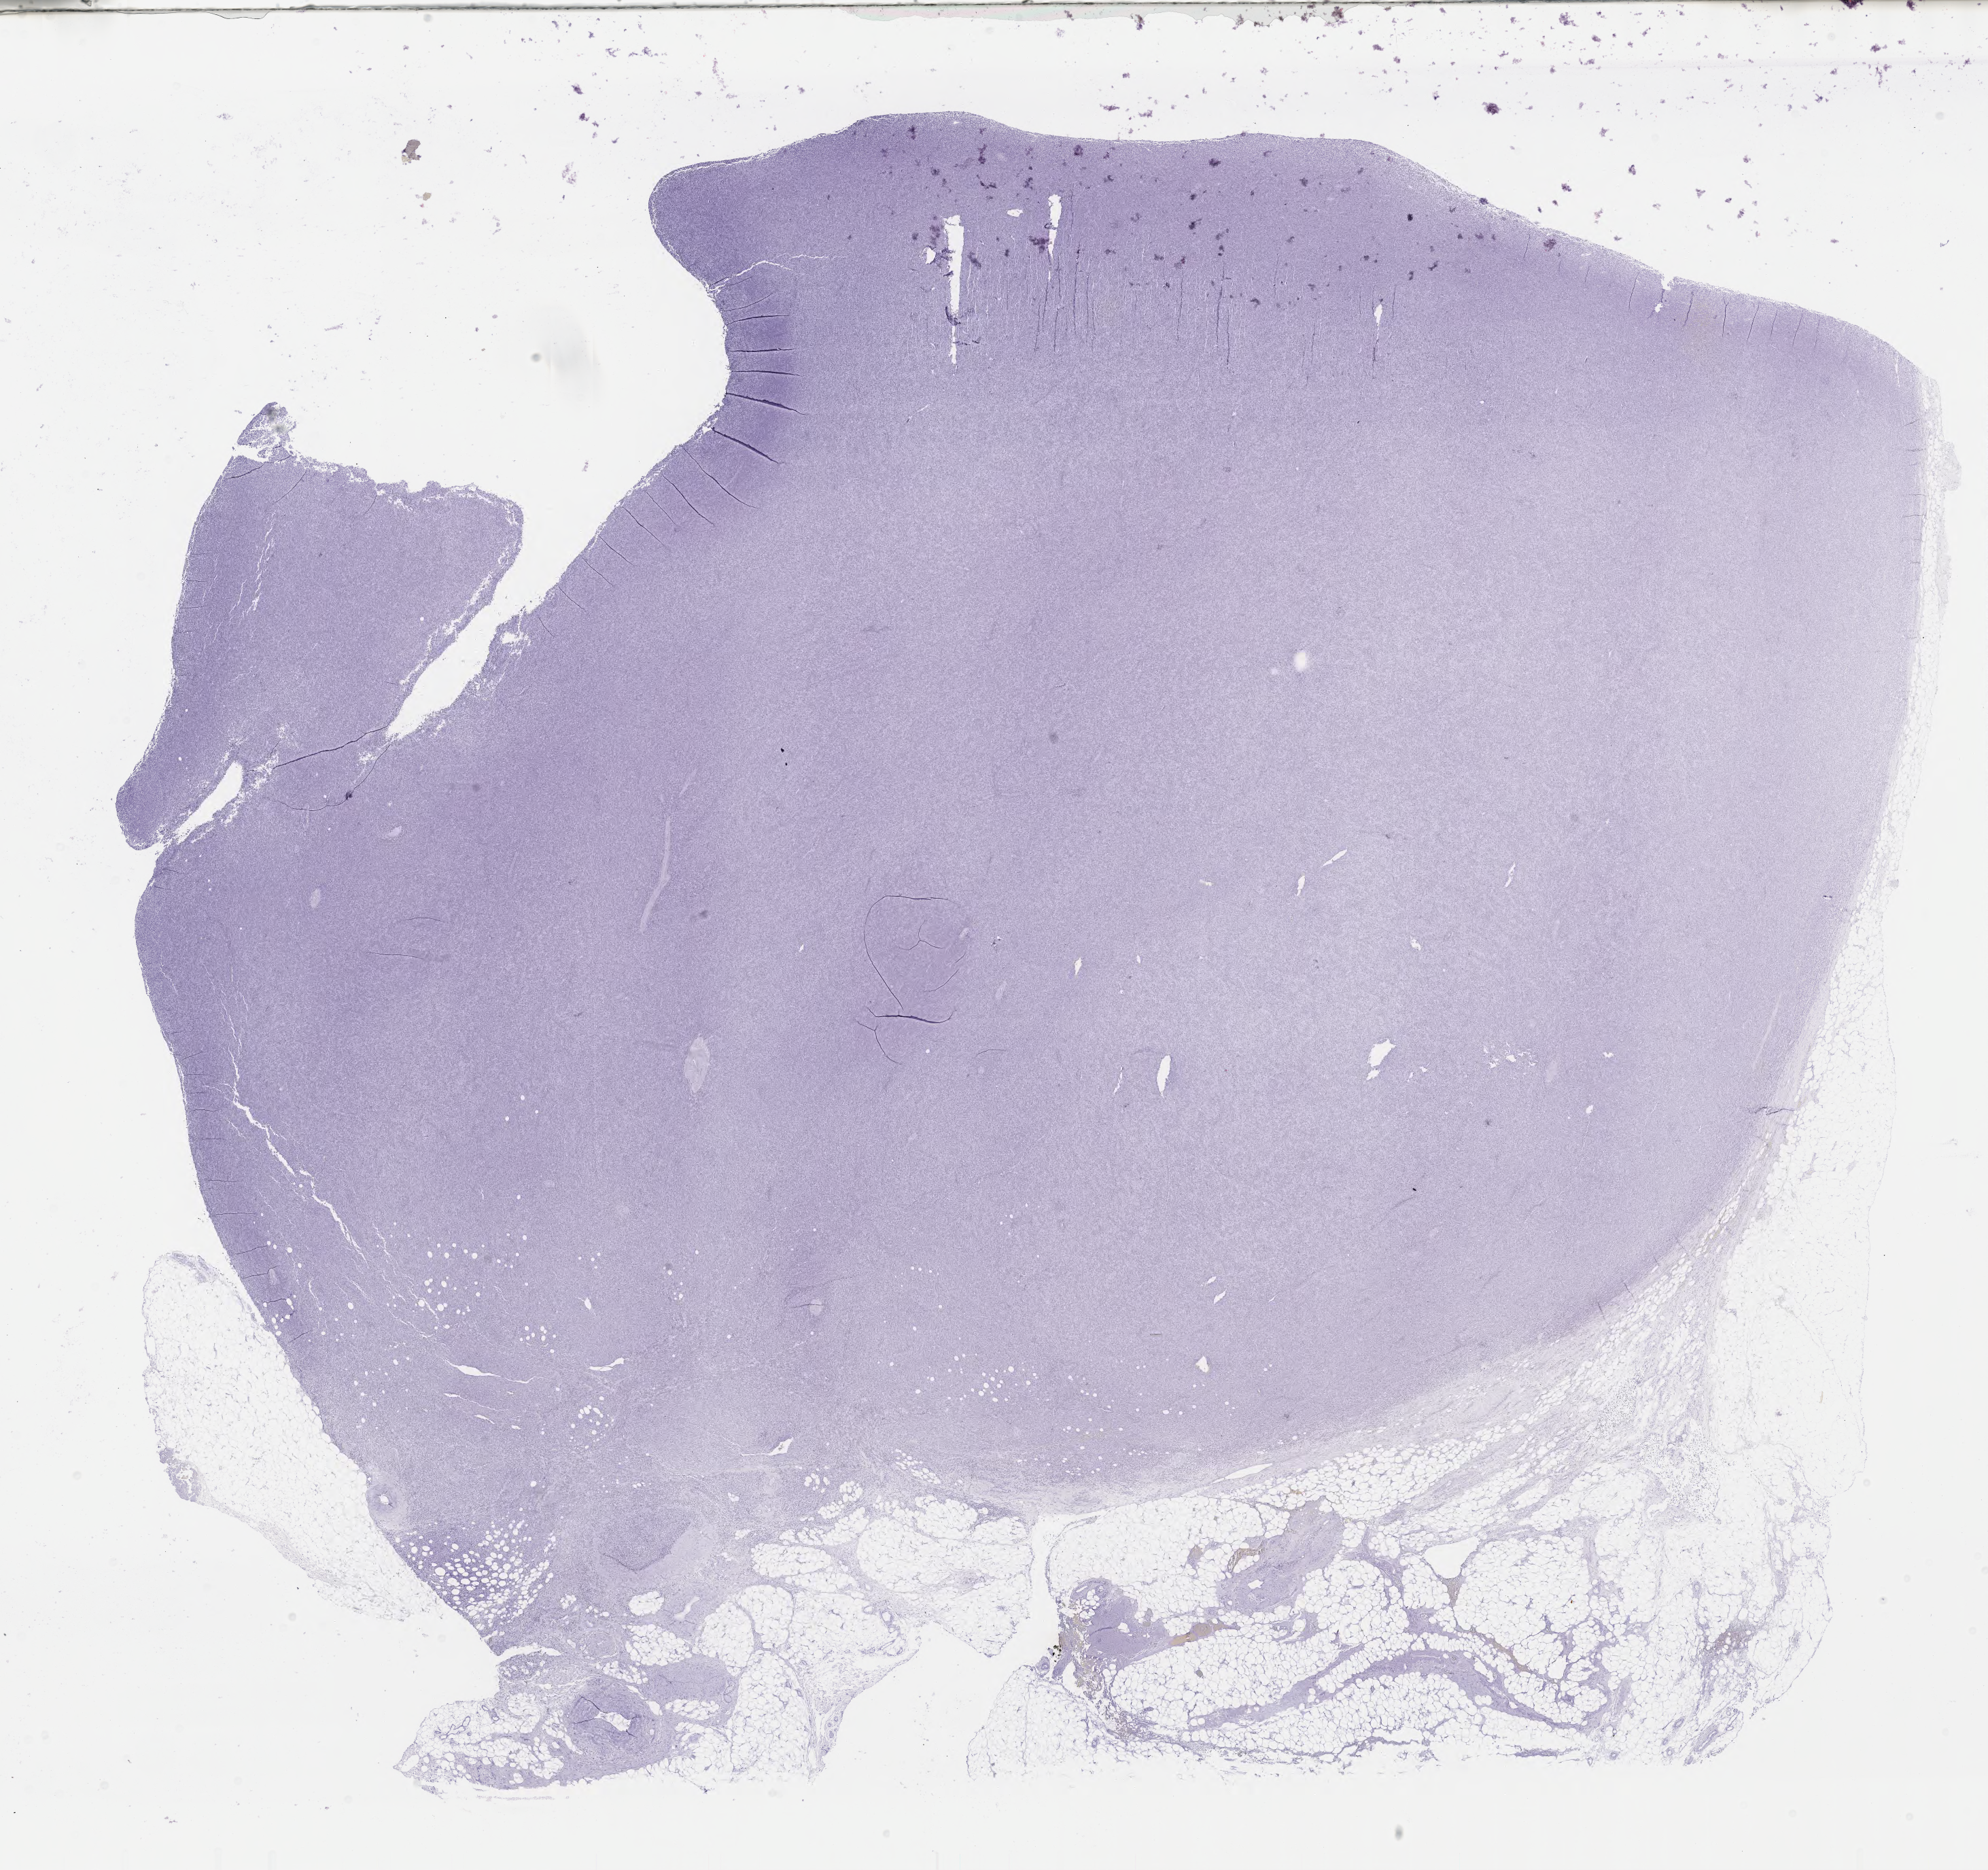
Whole-slide image, Epstein–Barr virus-encoded RNA (EBER) in-situ hybridisation — low-resolution overview of the scanned area, about 23.6 x 22.2 mm; tumor tissue; anatomic site: lymph node. Male patient, age 54 years.
Histologic diagnosis: Diffuse large B-cell lymphoma, NOS.